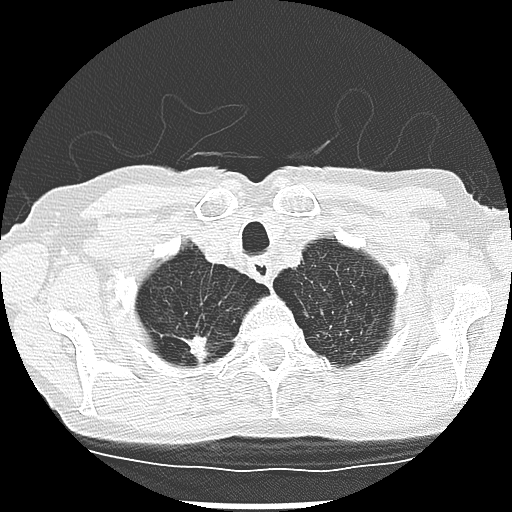
Low-dose screening chest CT, one axial slice; position 243 of 265 along the scan axis; reconstruction kernel LUNG; 120 kVp; lung window (W 1500 / L -600 HU); 2.5 mm slice thickness; 512 × 512 image matrix, field of view 300 × 300 mm.
Structures marked on this image (expert manual segmentation):
- lesion 2 (tumor, upper lobe of right lung): bounding box (x1, y1, x2, y2) in pixels: (186, 336, 209, 361)